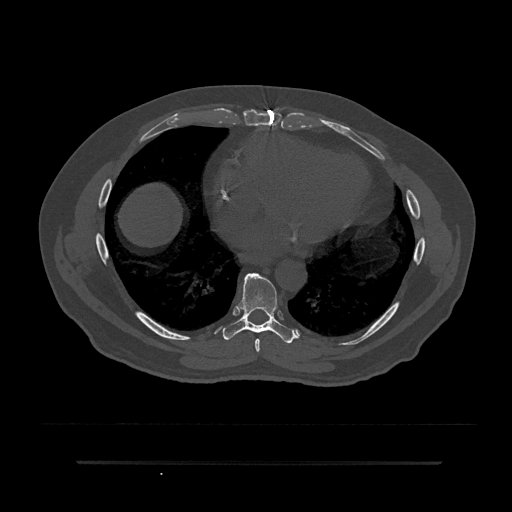
CT including the spine, one axial slice. Slice 437 of 797 in the series (ordered by position). Reconstruction kernel Br40s/3. 120 kVp. Bone window (W 1800 / L 400 HU). 512 × 512 image matrix, field of view 464 × 464 mm. Patient: male, 59 years. Case-level facts recorded for this patient, not image findings: primary cancer: bile ducts.
Structures marked on this image (semi-automatic segmentation, software-assisted and operator-edited):
- T7 vertebra: box from (x=255, y=338) to (x=260, y=353) px
- T8 vertebra: (x=223, y=273)–(x=296, y=344)